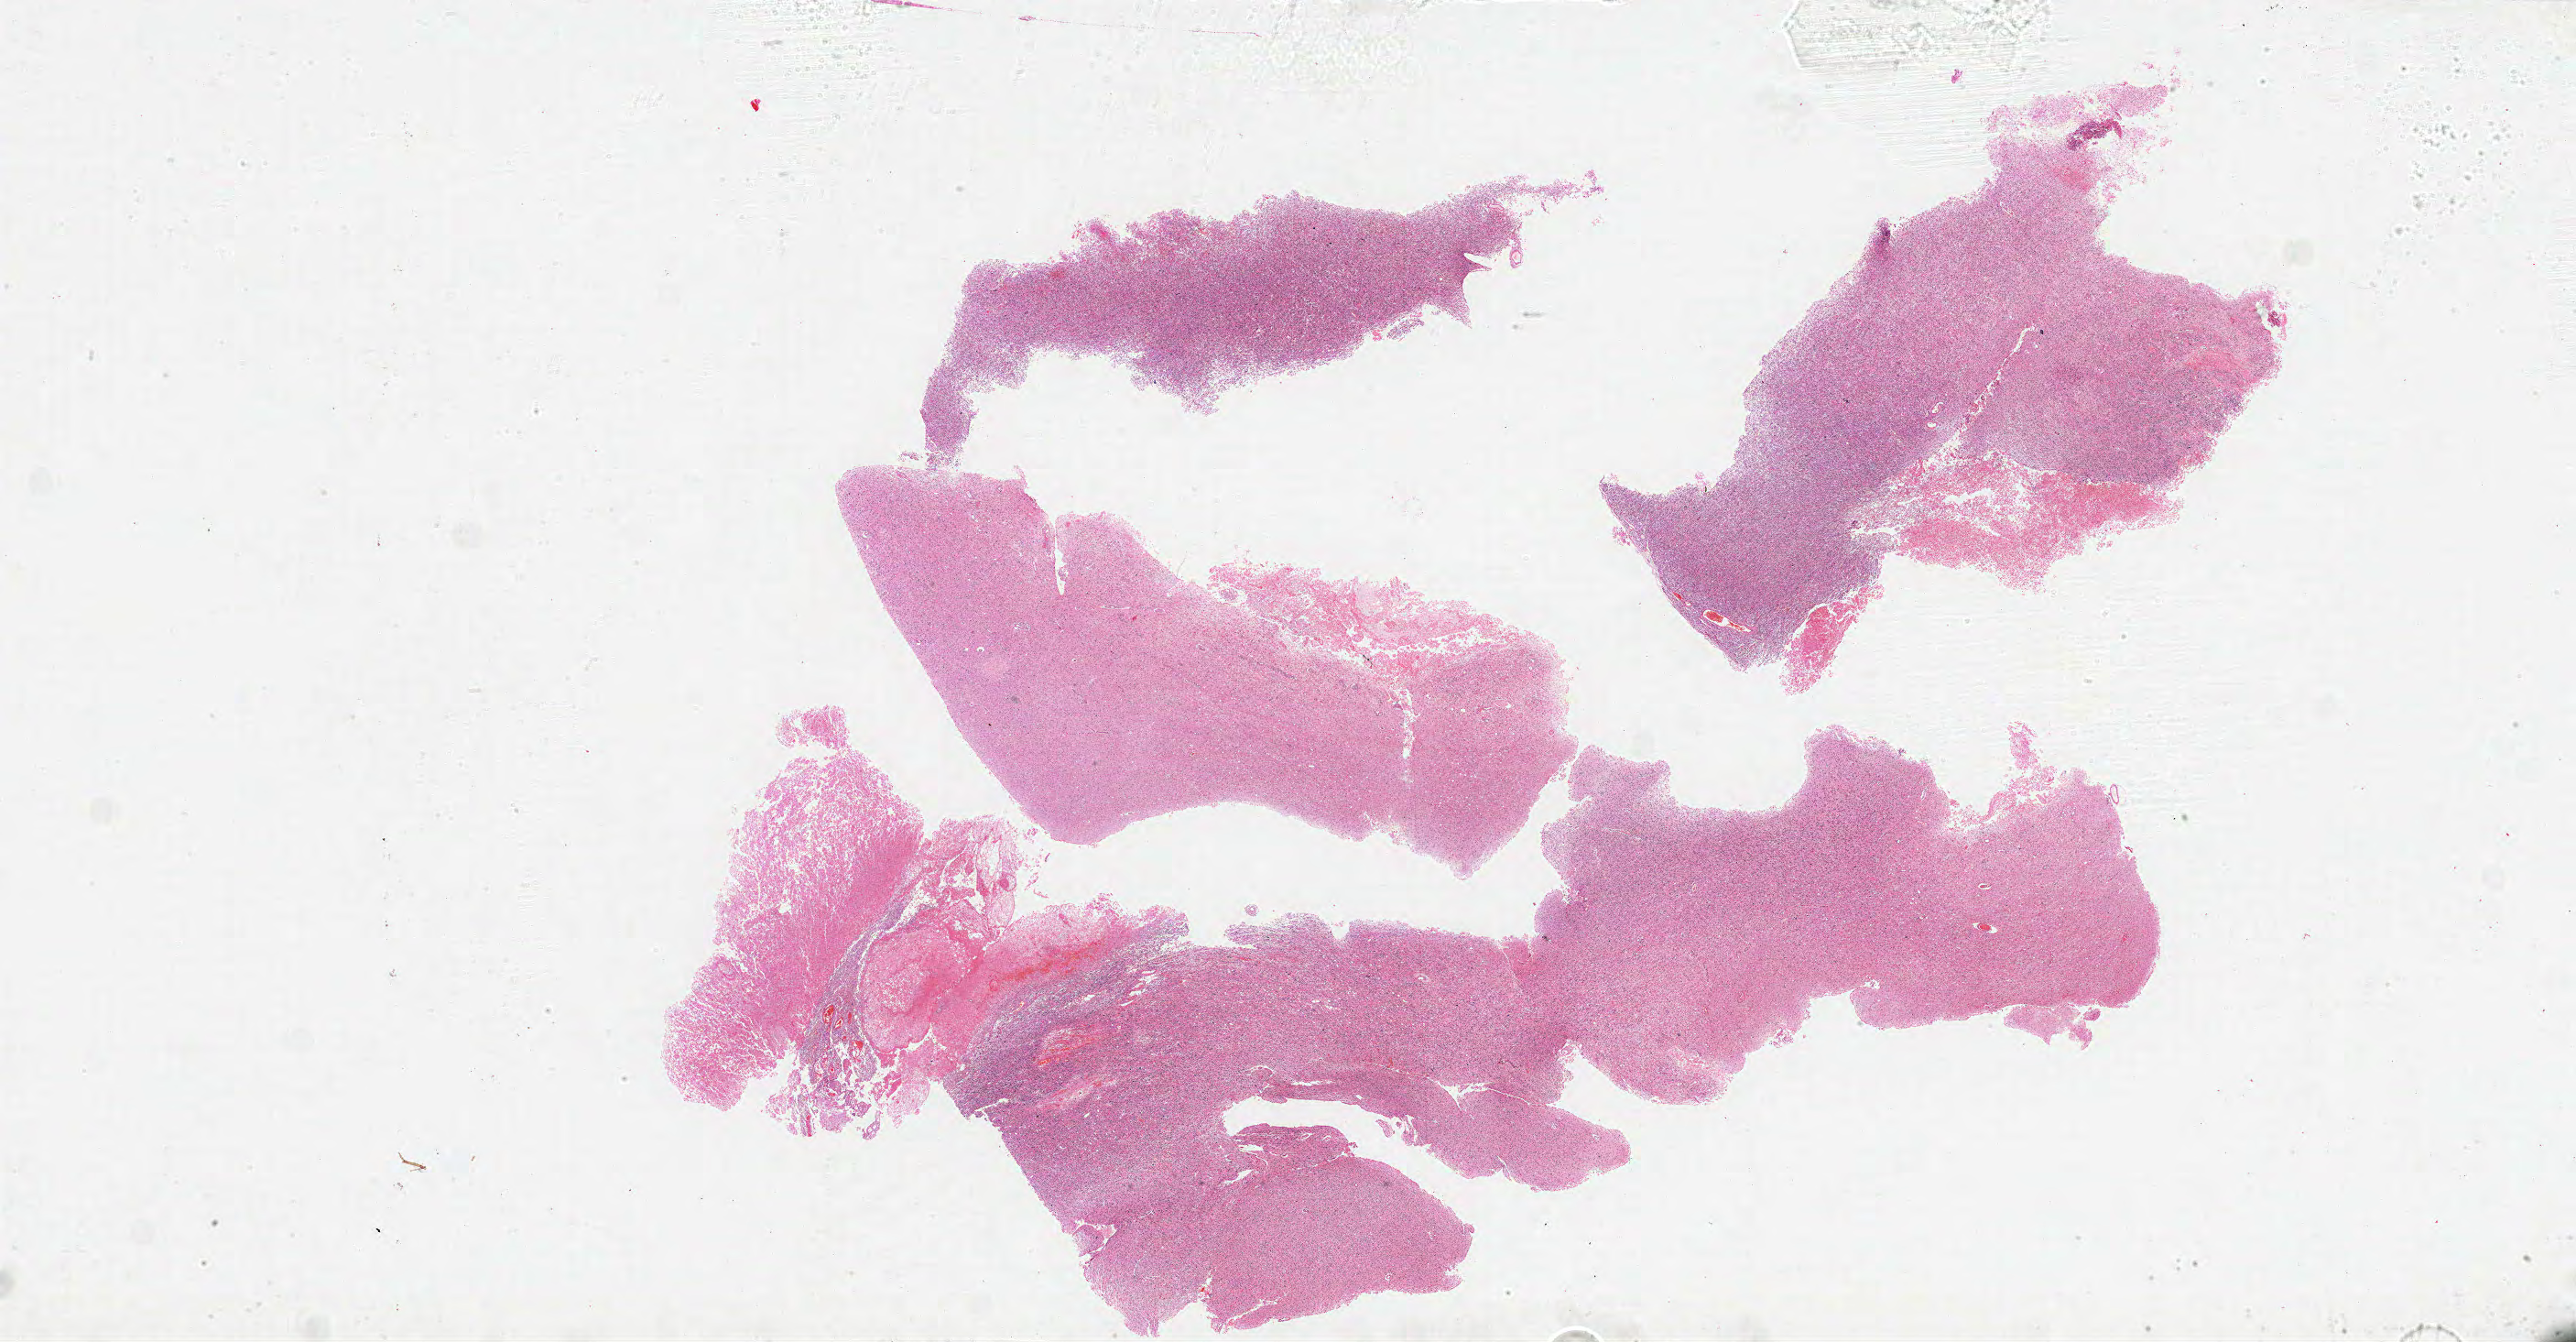
Digitized H&E tissue section (whole slide) — whole scanned area (about 45.0 x 23.4 mm, acquisition: 20x scan) shown as a low-resolution overview; formalin-fixed paraffin-embedded (FFPE) diagnostic section; brain, primary tumour sample. Female patient; age at initial diagnosis 38 years.
- diagnosis: Glioblastoma